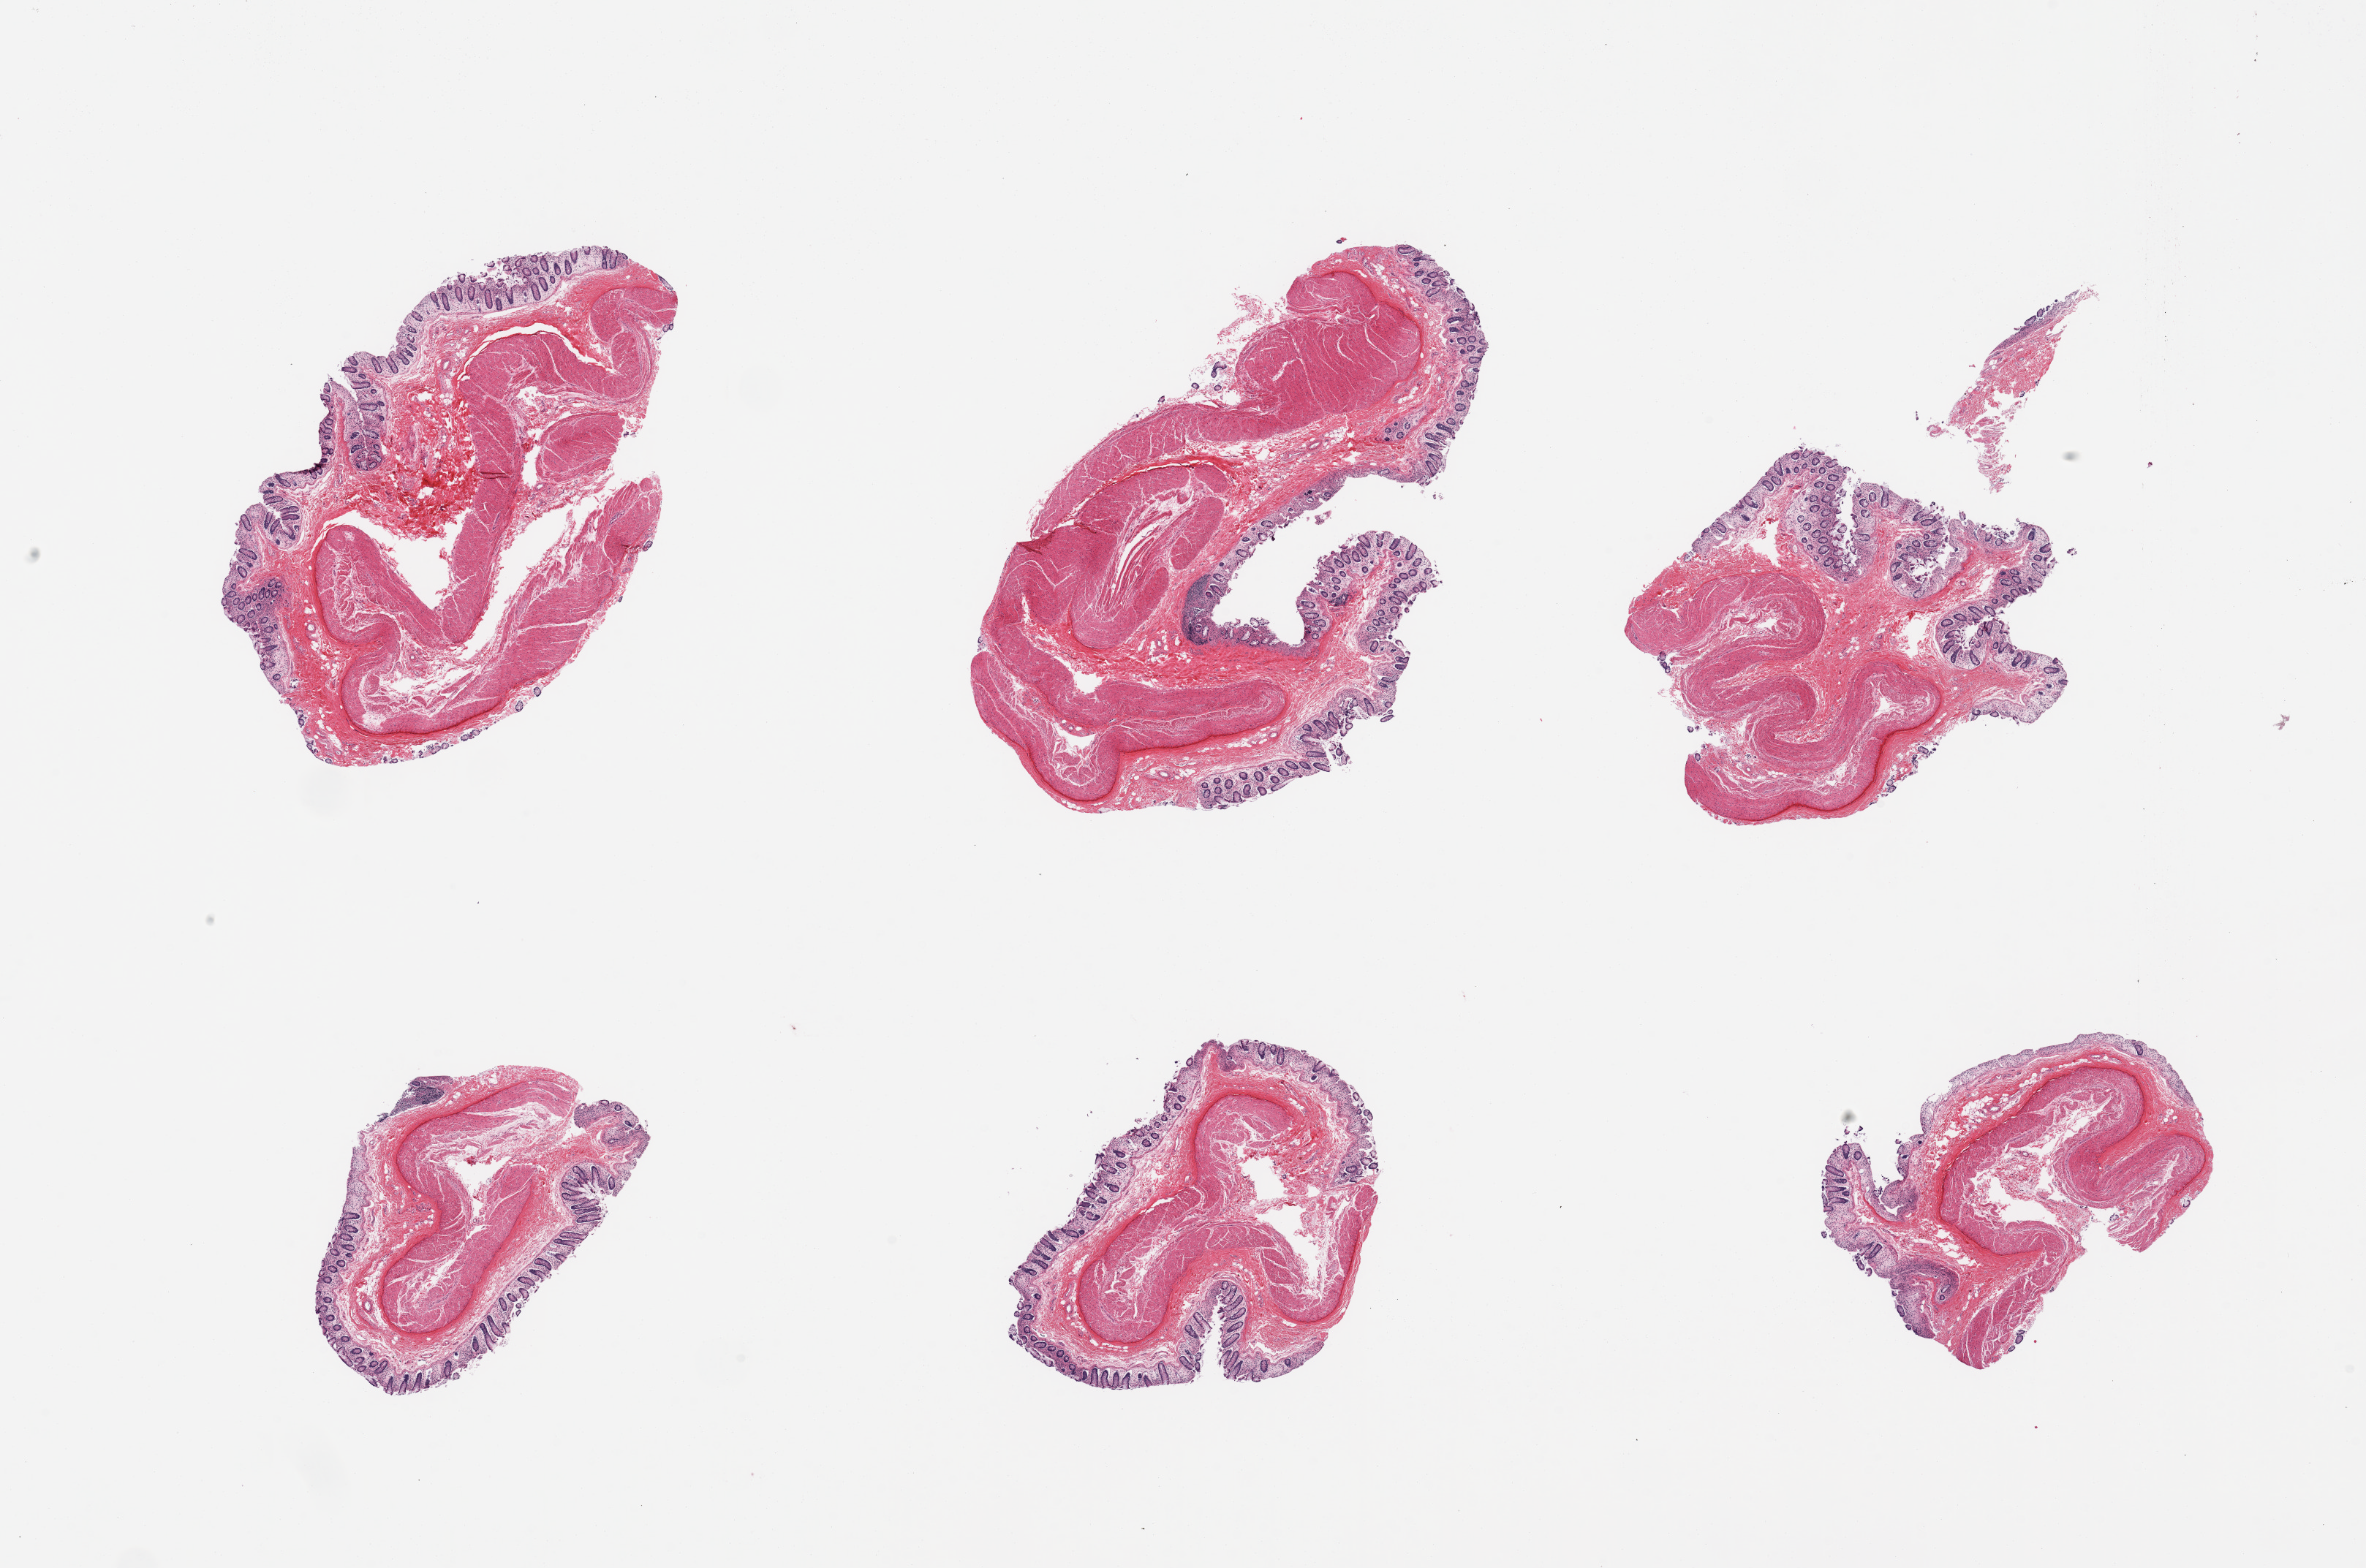
Whole-slide image, H&E stain, brightfield — a low-resolution overview of the entire scanned area, about 25.6 x 17.0 mm, PAXgene-fixed, paraffin-embedded tissue, sampled site (target tissue): transverse colon, donor tissue sample. Male donor.
- review note (as recorded): 6 pieces, glandular mucosa up to ~0.2mm, partially sloughing